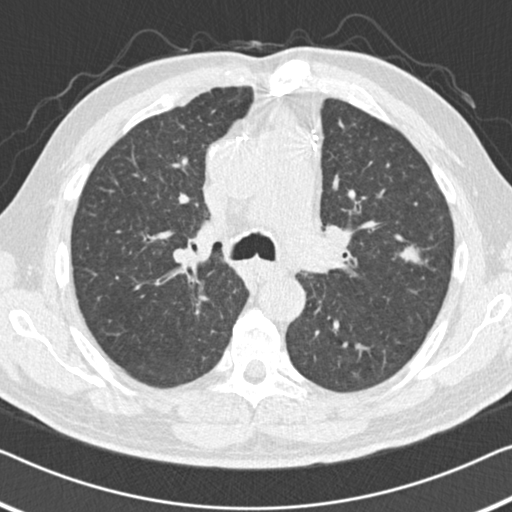
Low-dose screening chest CT, axial slice. First (baseline) screen. Lung window (W 1500 / L -600 HU). Slice 55 of 155 in the series. 512 × 512 image matrix, field of view 332 × 332 mm. Male participant, aged 64 years at enrolment.
Expert-annotated lung lesion, bounding box (x1, y1, x2, y2) in pixels: (383, 229, 439, 281). The screening reader recorded 2 non-calcified nodules or masses ≥4 mm on this exam (left upper lobe, right middle lobe); which of them this box marks is not recorded. Official screen result: positive, change unspecified: nodule(s) >= 4 mm or enlarging nodule(s), mass(es), or other non-specific abnormalities suspicious for lung cancer.